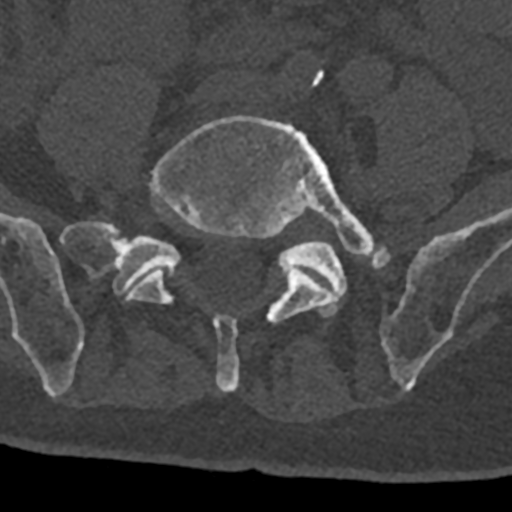
CT including the spine, one axial slice. Position 185 of 797 along the scan axis. Reconstruction kernel Br40s/3. 120 kVp. Bone window (W 1800 / L 400 HU). 512 × 512 image matrix. Male patient, age 74 years. Case-level facts recorded for this patient, not image findings: primary cancer: renal; vertebrae with lytic lesions (as recorded): T10, L1, L2, L3, L4, L5.
Structures marked on this image (semi-automatically segmented with operator editing):
- L4 vertebra: bounding box <312,70,324,87> (left, top, right, bottom; pixels)
- L5 vertebra: <127,115,376,392>